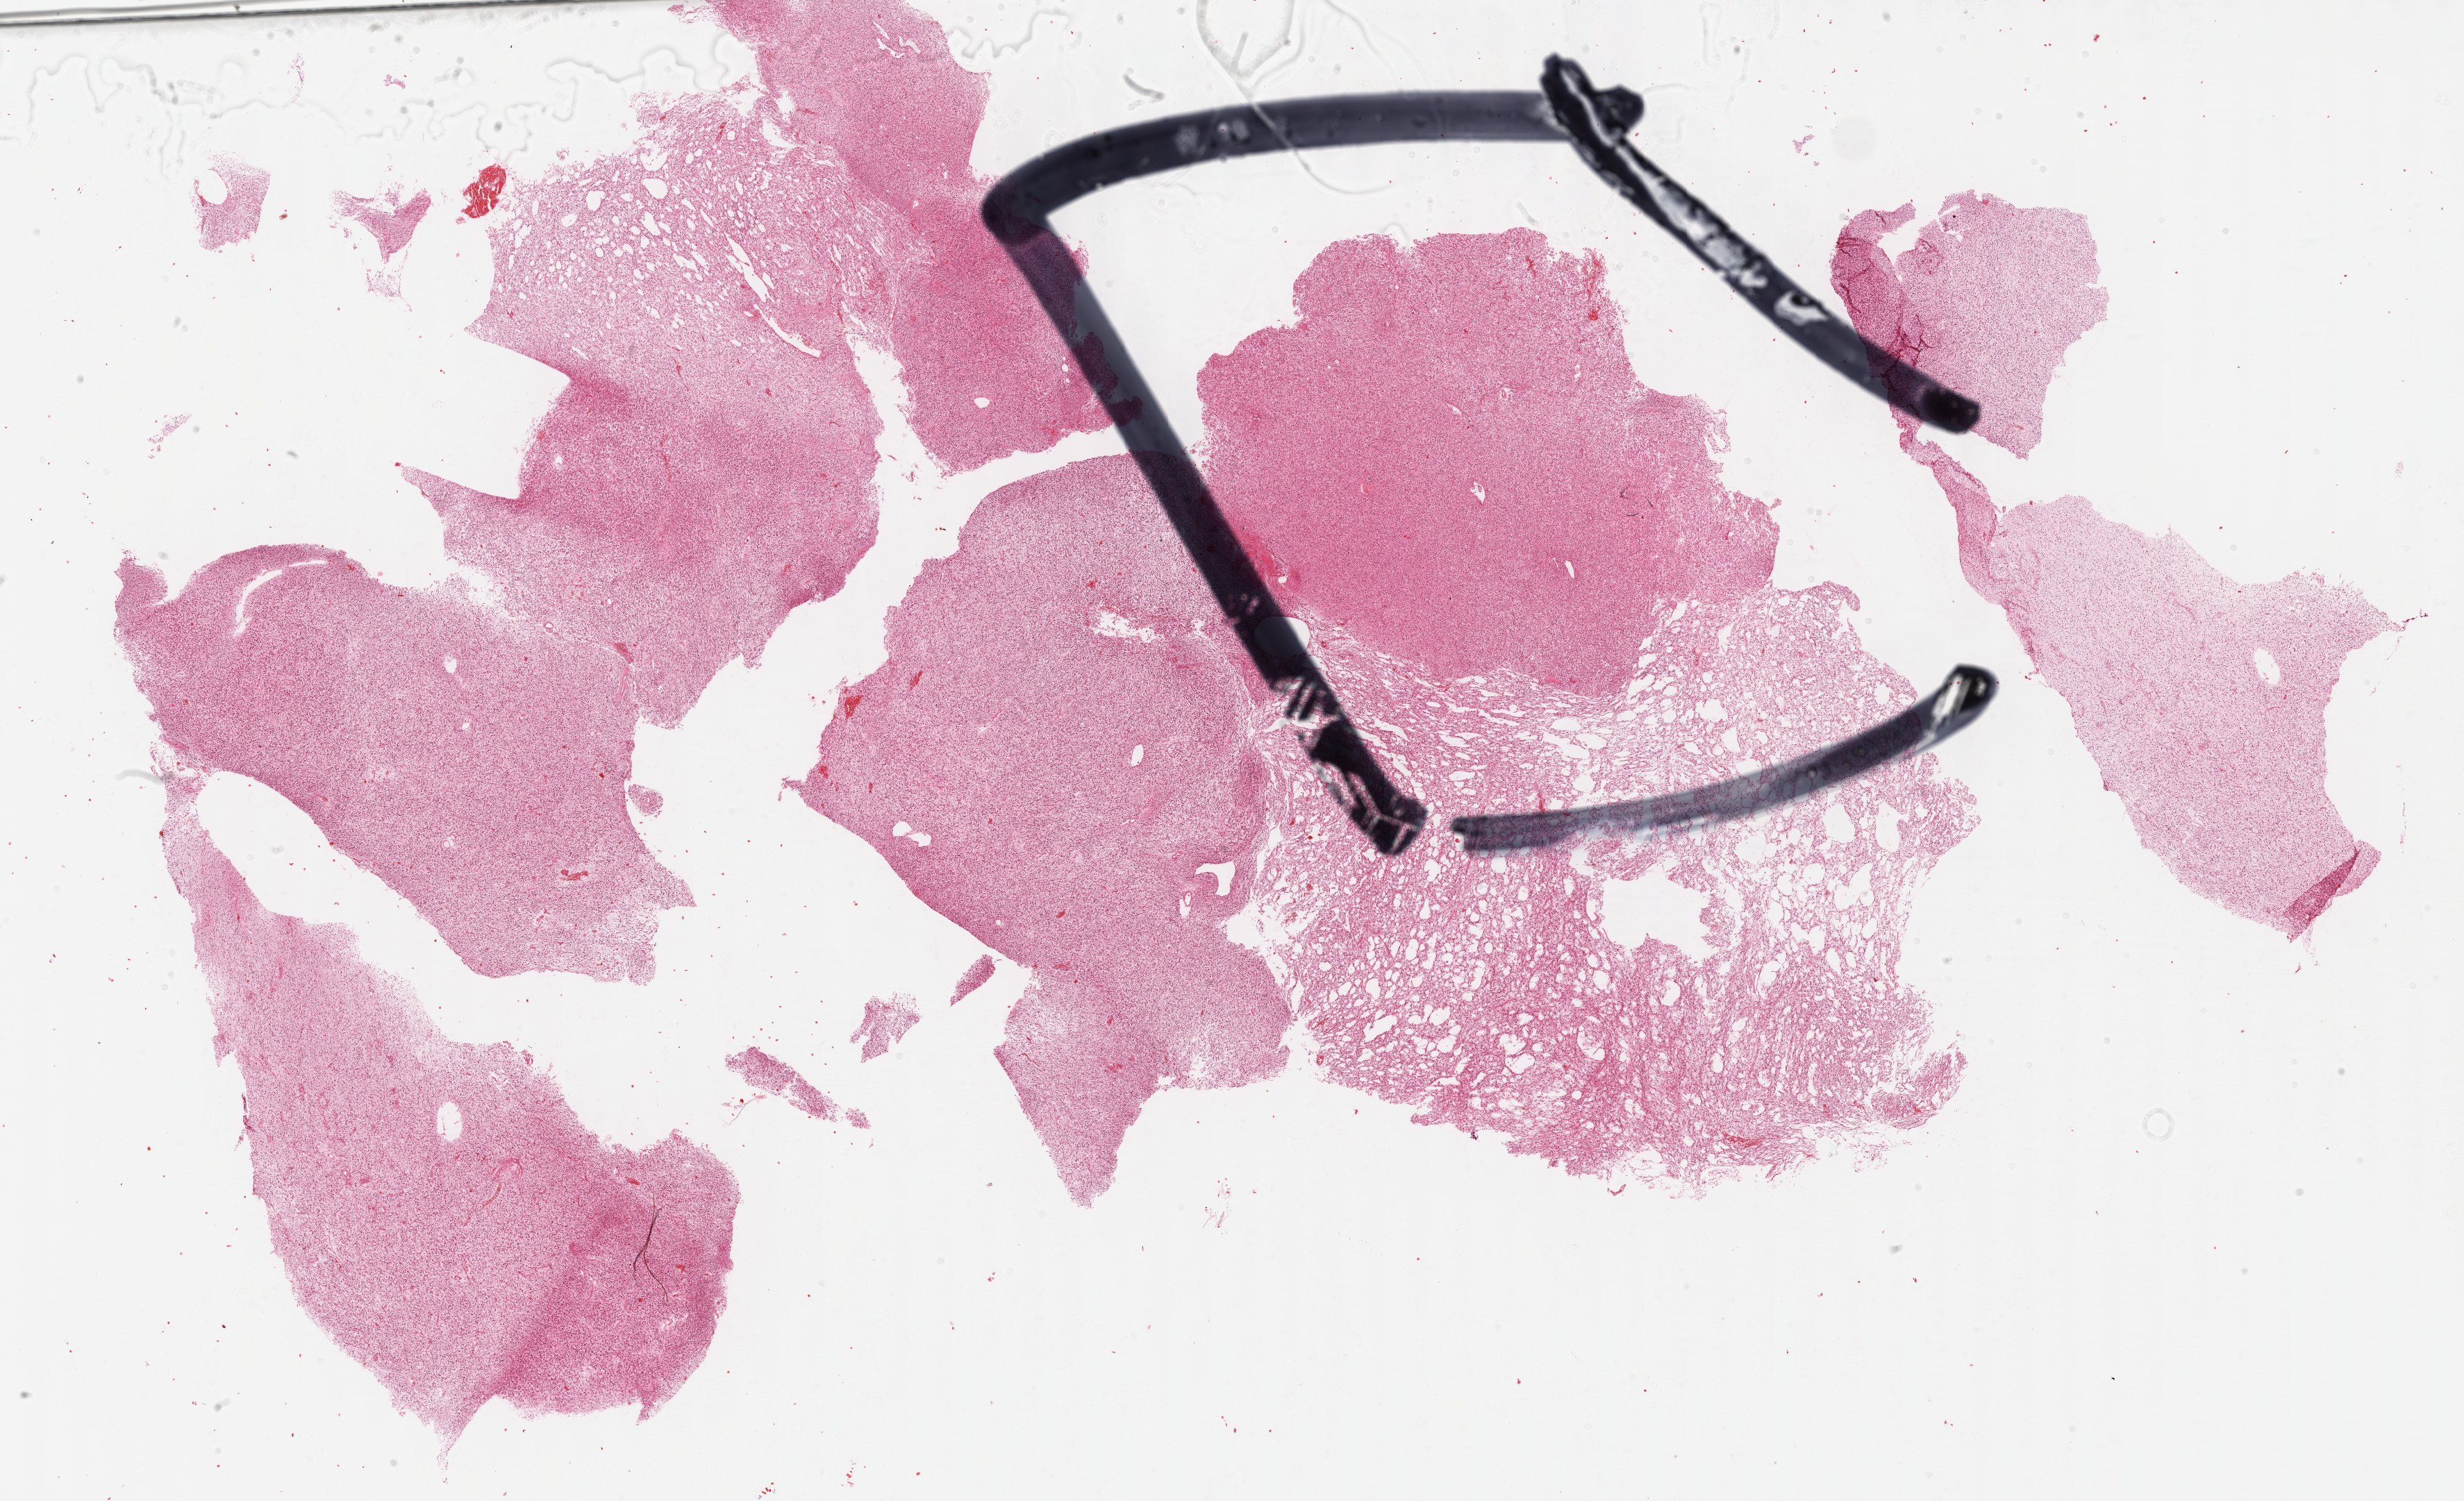
Digitized Hematoxylin and eosin (H&E) stained tissue section (whole slide) — a low-resolution overview of the entire scanned area, about 28.7 x 17.5 mm, formalin-fixed paraffin-embedded (FFPE) diagnostic section, sample: primary tumour, brain. Female, age 39 years at initial diagnosis. Histologic grade: G2 (moderately differentiated).
Laterality: left. Pathologic diagnosis: Astrocytoma, NOS (cerebrum).